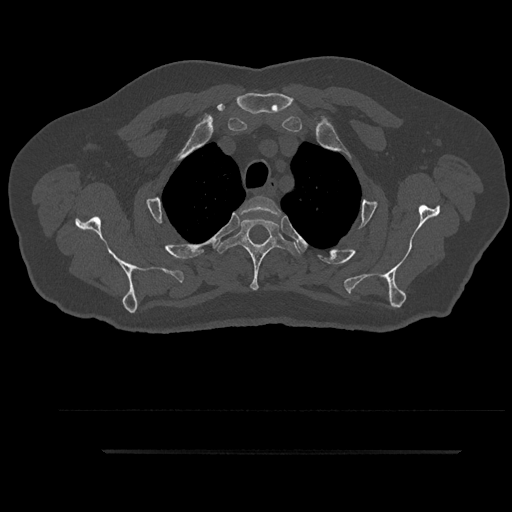
CT including the spine, one axial slice. Position 724 of 797 along the scan axis. 120 kVp. Bone window (W 1800 / L 400 HU). 0.5 mm slice thickness. 512 × 512 image matrix. Patient: male, 63 years. Case-level facts recorded for this patient, not image findings: primary cancer: renal; vertebrae with lytic lesions (as recorded): T8.
Structures marked on this image (semi-automatic segmentation, software-assisted and operator-edited):
- T2 vertebra: bounding box <239,196,281,220> (left, top, right, bottom; pixels)
- T3 vertebra: <217,218,300,291>